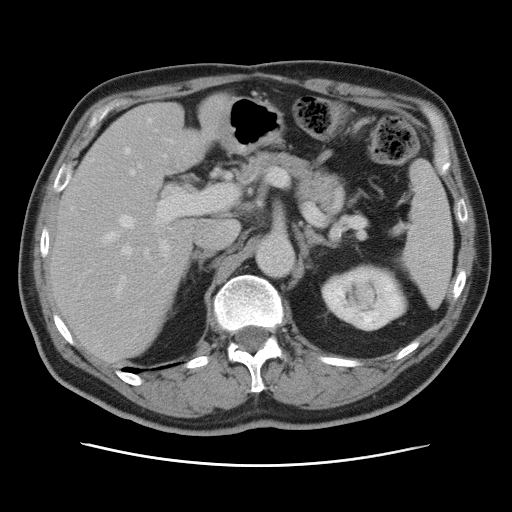
Contrast-enhanced abdominal CT, one axial slice. Position 47 of 80 along the scan axis. 120 kVp. Intravenous contrast given. Soft-tissue window (W 400 / L 40 HU). 5 mm slice thickness. 512 × 512 image matrix, field of view 370 × 370 mm. Male patient, age 69 years. From the clinical record (not read from this slice): diagnosis: colorectal cancer liver metastases, imaged before liver resection; multiple liver metastases: no.
Outlined on this slice (manually delineated by an expert):
- hepatic veins: bounding box <104,148,167,294> (left, top, right, bottom; pixels)
- liver: <50,96,230,359>
- planned liver remnant (the part of the liver to remain after resection): <50,95,229,359>
- portal vein (with intrahepatic branches): <121,140,205,257>